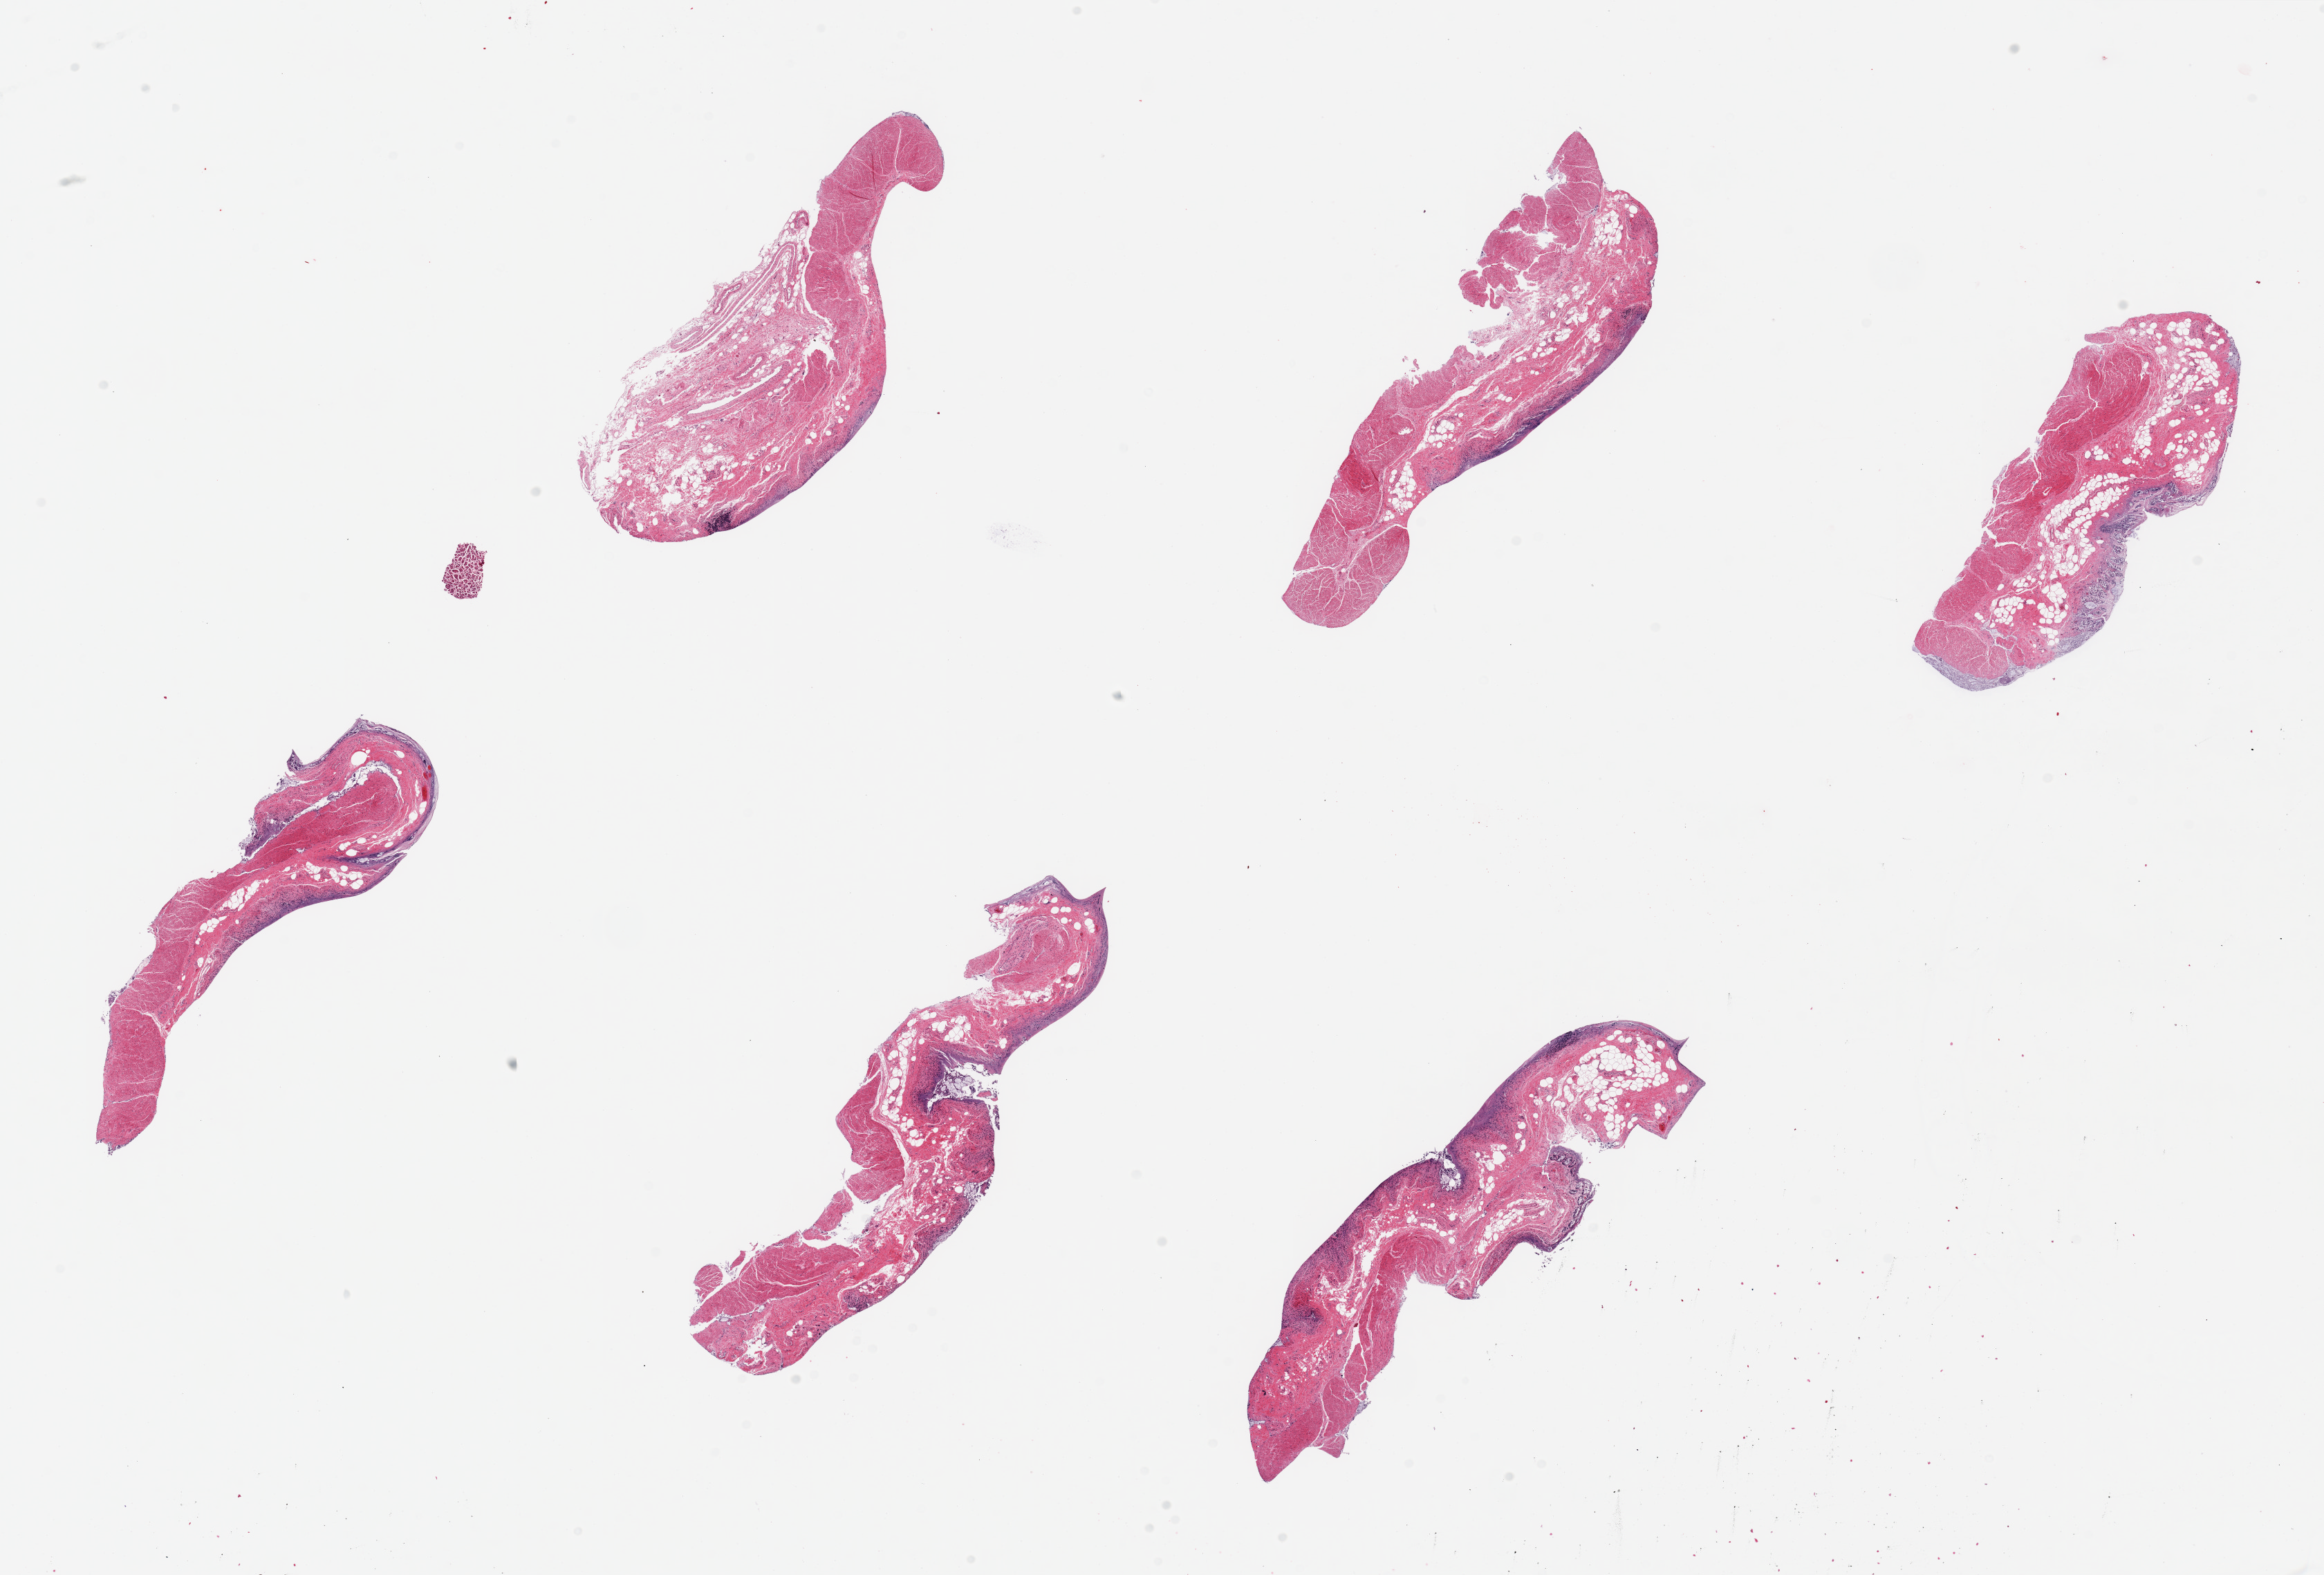
Haematoxylin and eosin whole-slide image — a low-resolution overview of the entire scanned area, about 26.6 x 18.0 mm; PAXgene-fixed paraffin-embedded (PFPE) section; section of sigmoid colon (target tissue); tissue donor sample. Male donor.
Review note (as recorded): 6 pieces, up to 7x2mm; 20-30% fat, mainly muscularis, trace autolyzed mucosa.